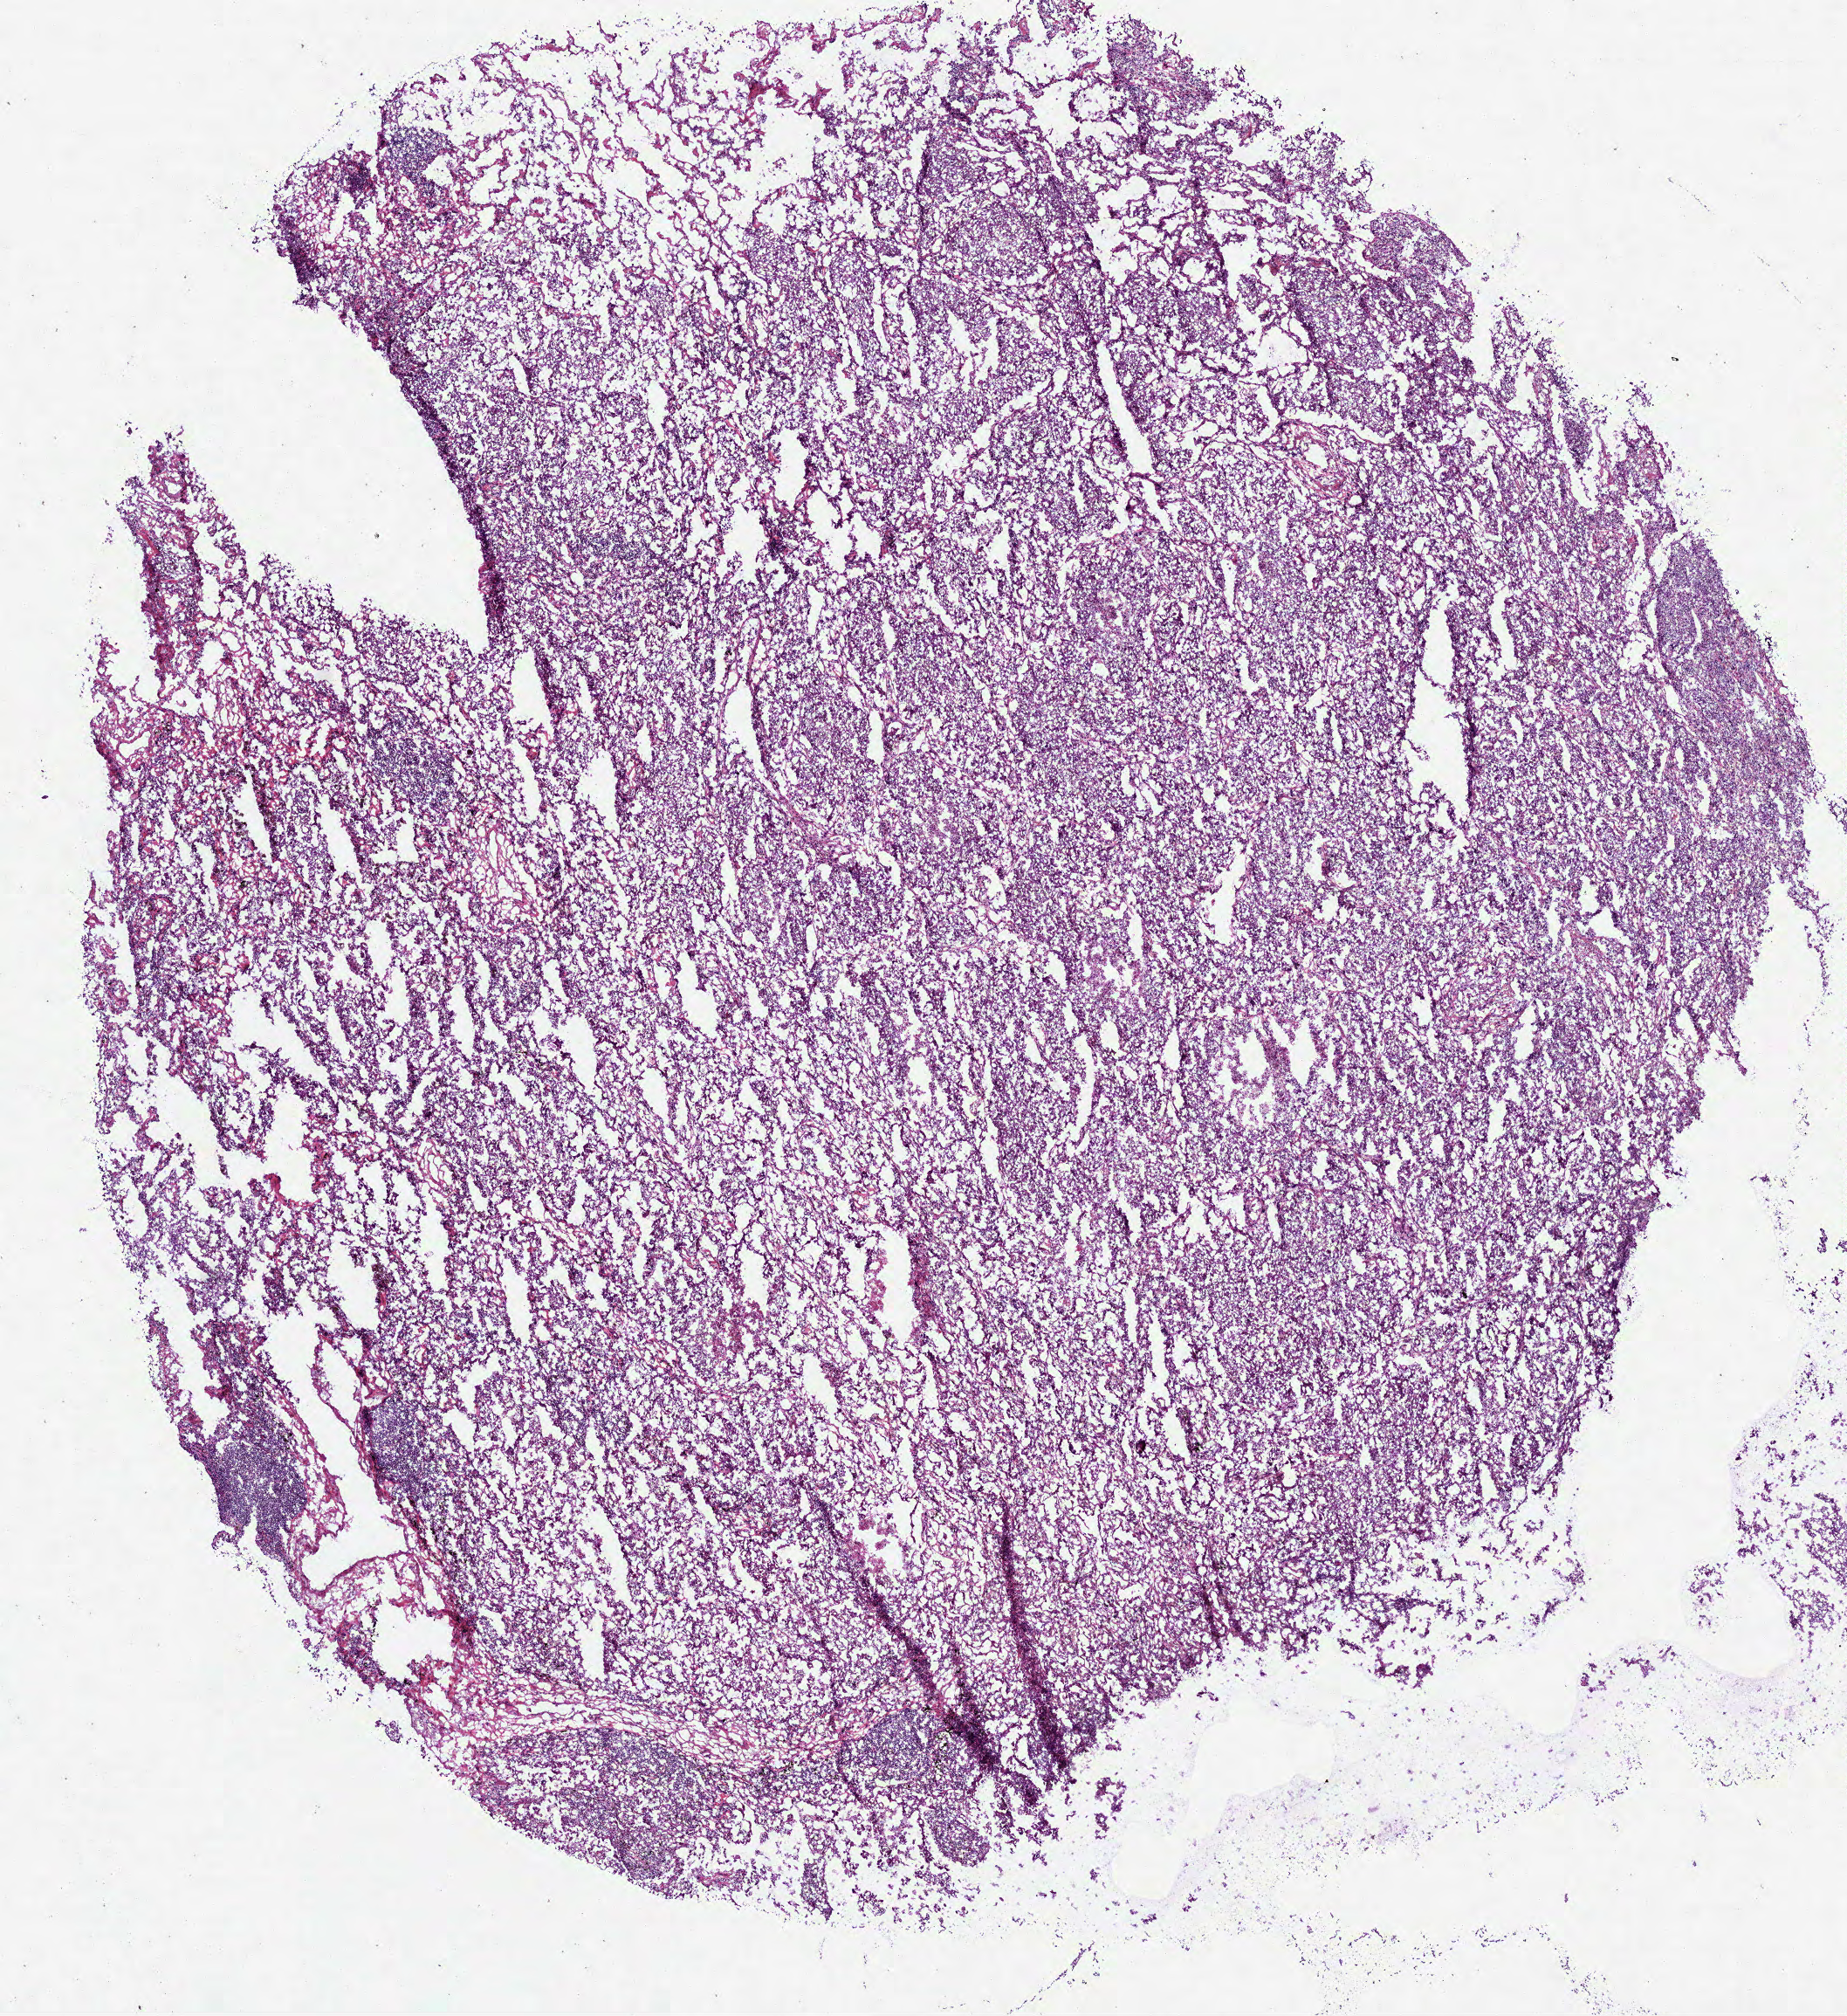
H&E whole-slide image — a low-resolution overview of the entire scanned area, about 8.5 x 9.3 mm (from a 40x scan). Frozen section from the bottom of the tissue portion. Lung, primary tumour sample. Female, age 55 years at initial diagnosis. Composition of this section per pathologist review: tumour cells 94%, tumour nuclei 71%, normal cells 0%, stromal cells 0%, necrosis 6%. Infiltration values recorded for this section: lymphocyte infiltration 10%, monocyte infiltration 0%, neutrophil infiltration 5%.
AJCC pathologic stage: IIIA (7th edition). Pathologic diagnosis: Adenocarcinoma, NOS. Laterality: right.